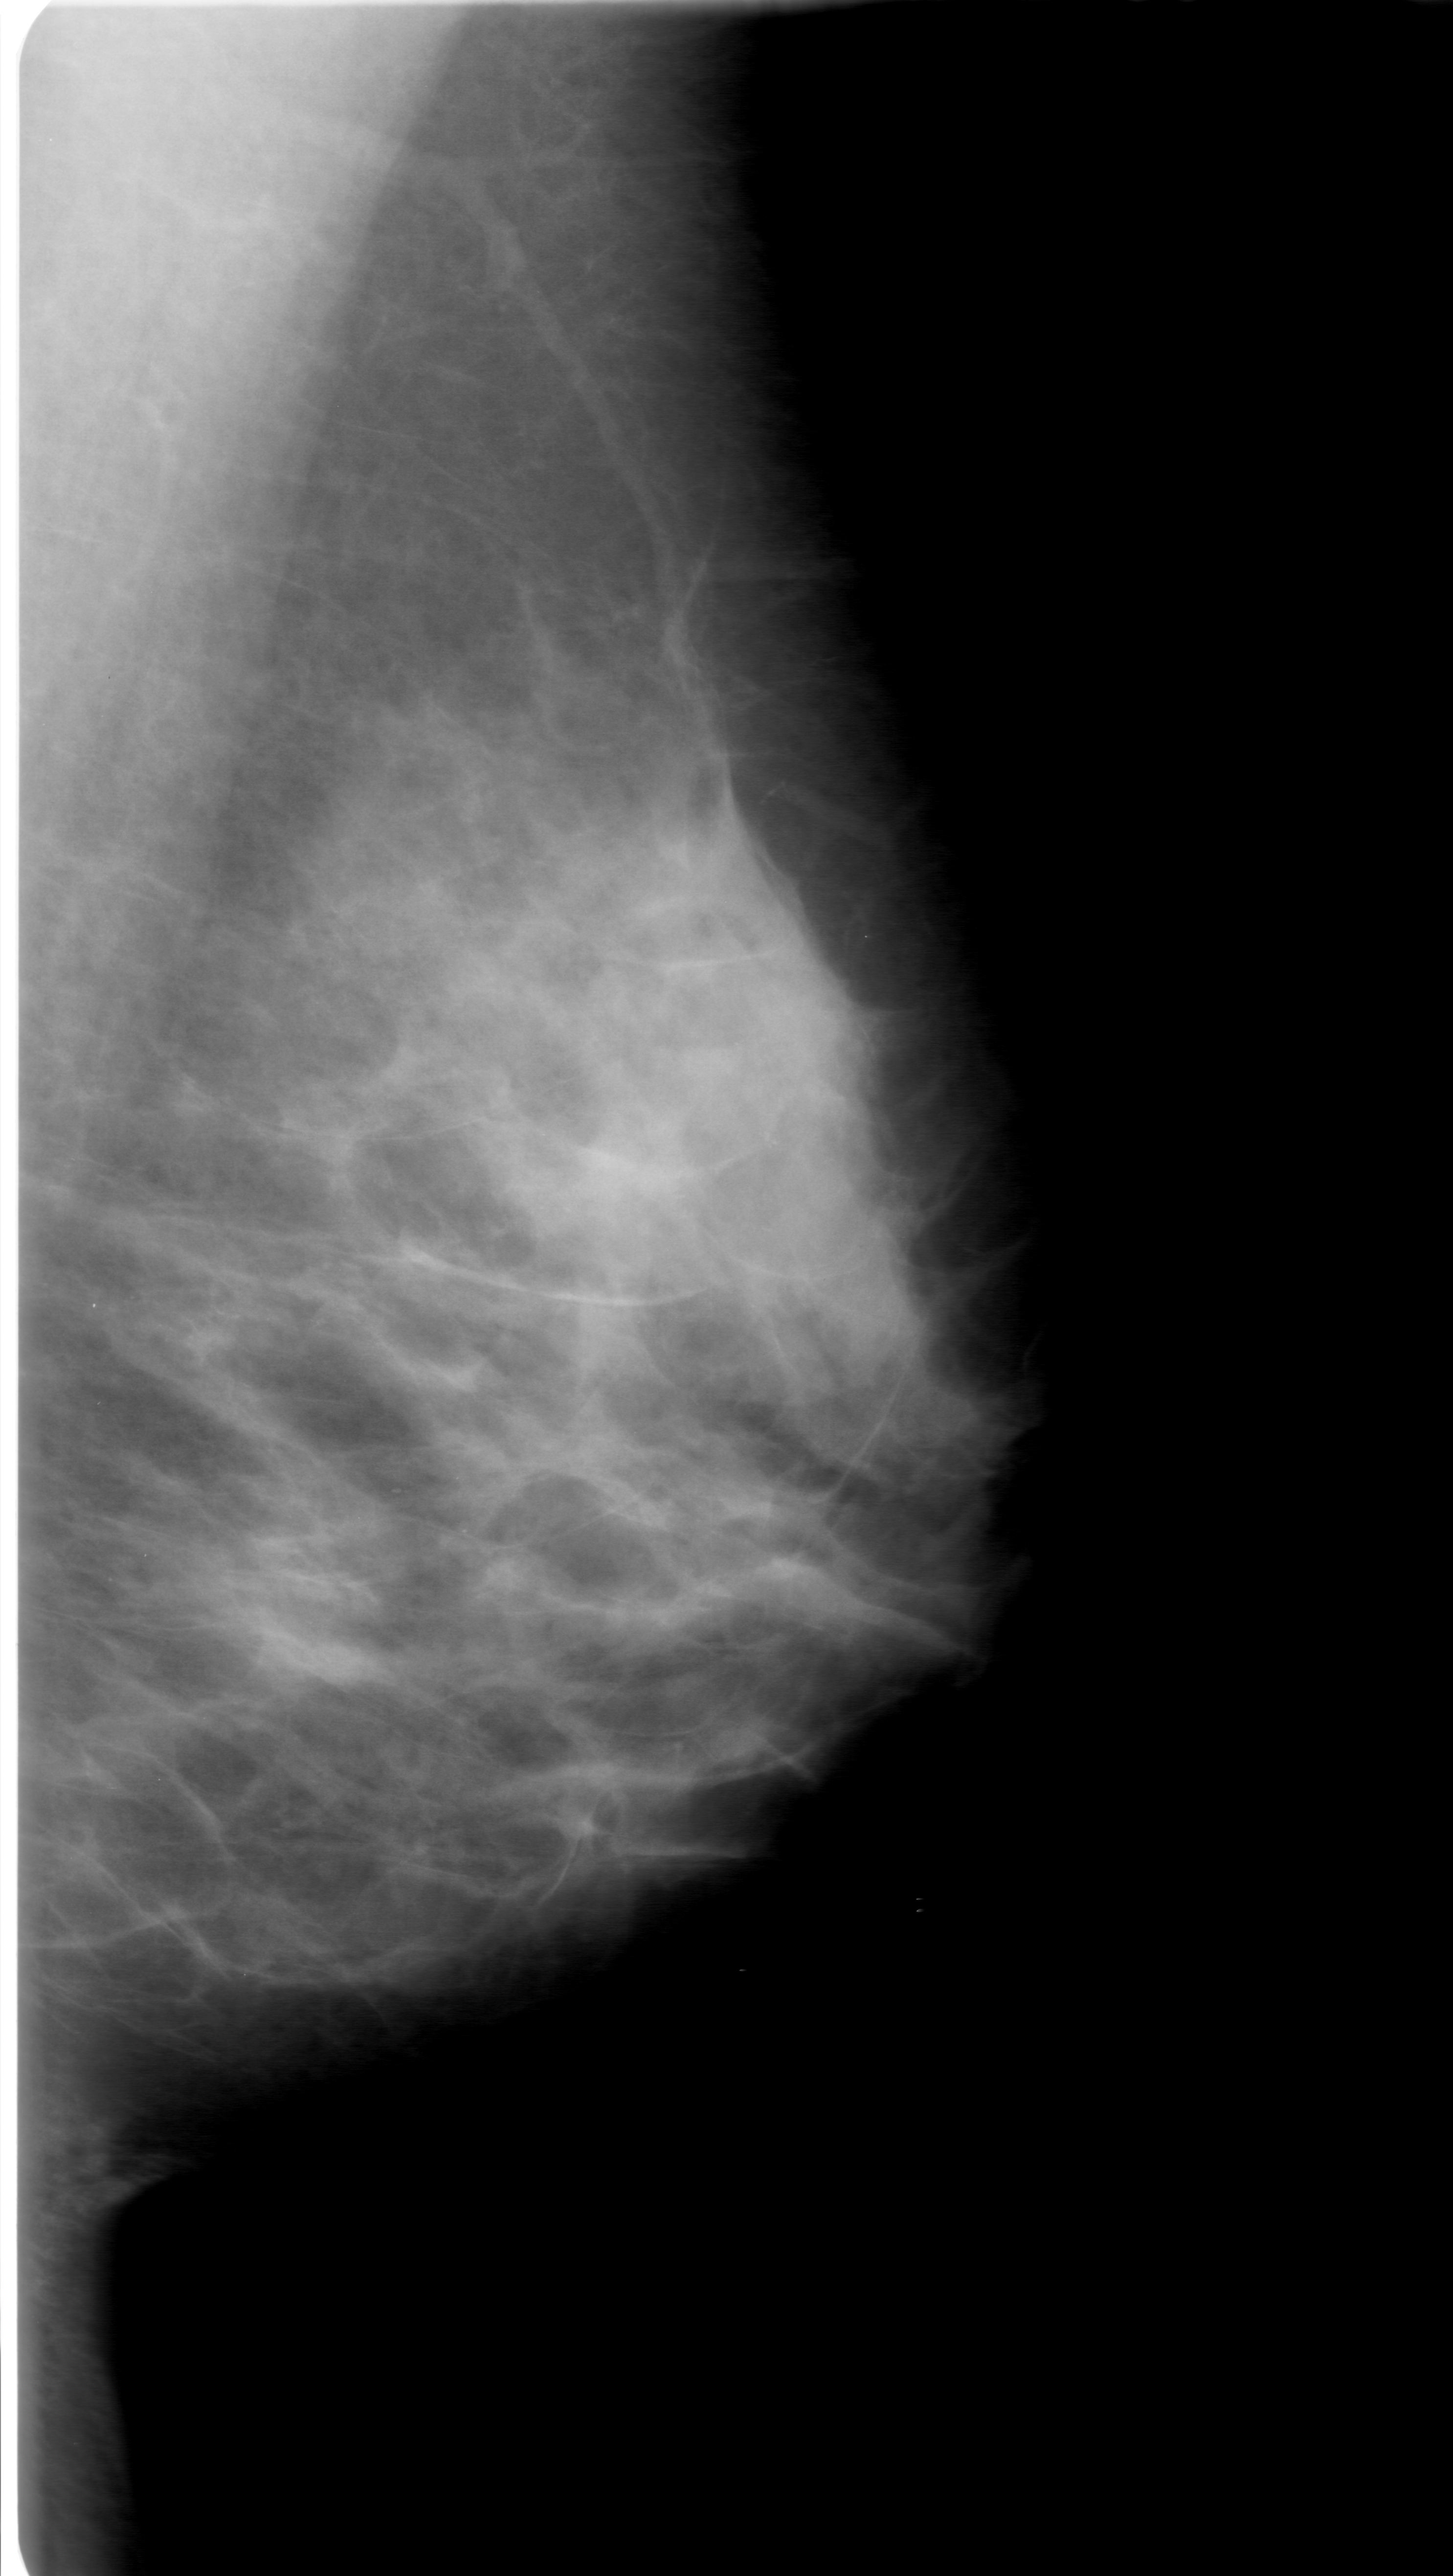
Scanned film-screen mammogram. Left breast. Mediolateral oblique (MLO) view. BI-RADS breast density category 3 (scale 1–4). 1453 × 2576 image matrix.
Expert-marked regions of interest on this film, with their recorded descriptors:
- calcifications, morphology amorphous, distribution segmental; BI-RADS assessment category 0; subtlety rating 1 on a 1 (subtle) to 5 (obvious) scale; pathology (as recorded): benign: bounding box [x1, y1, x2, y2] px = [22, 1020, 894, 1388]